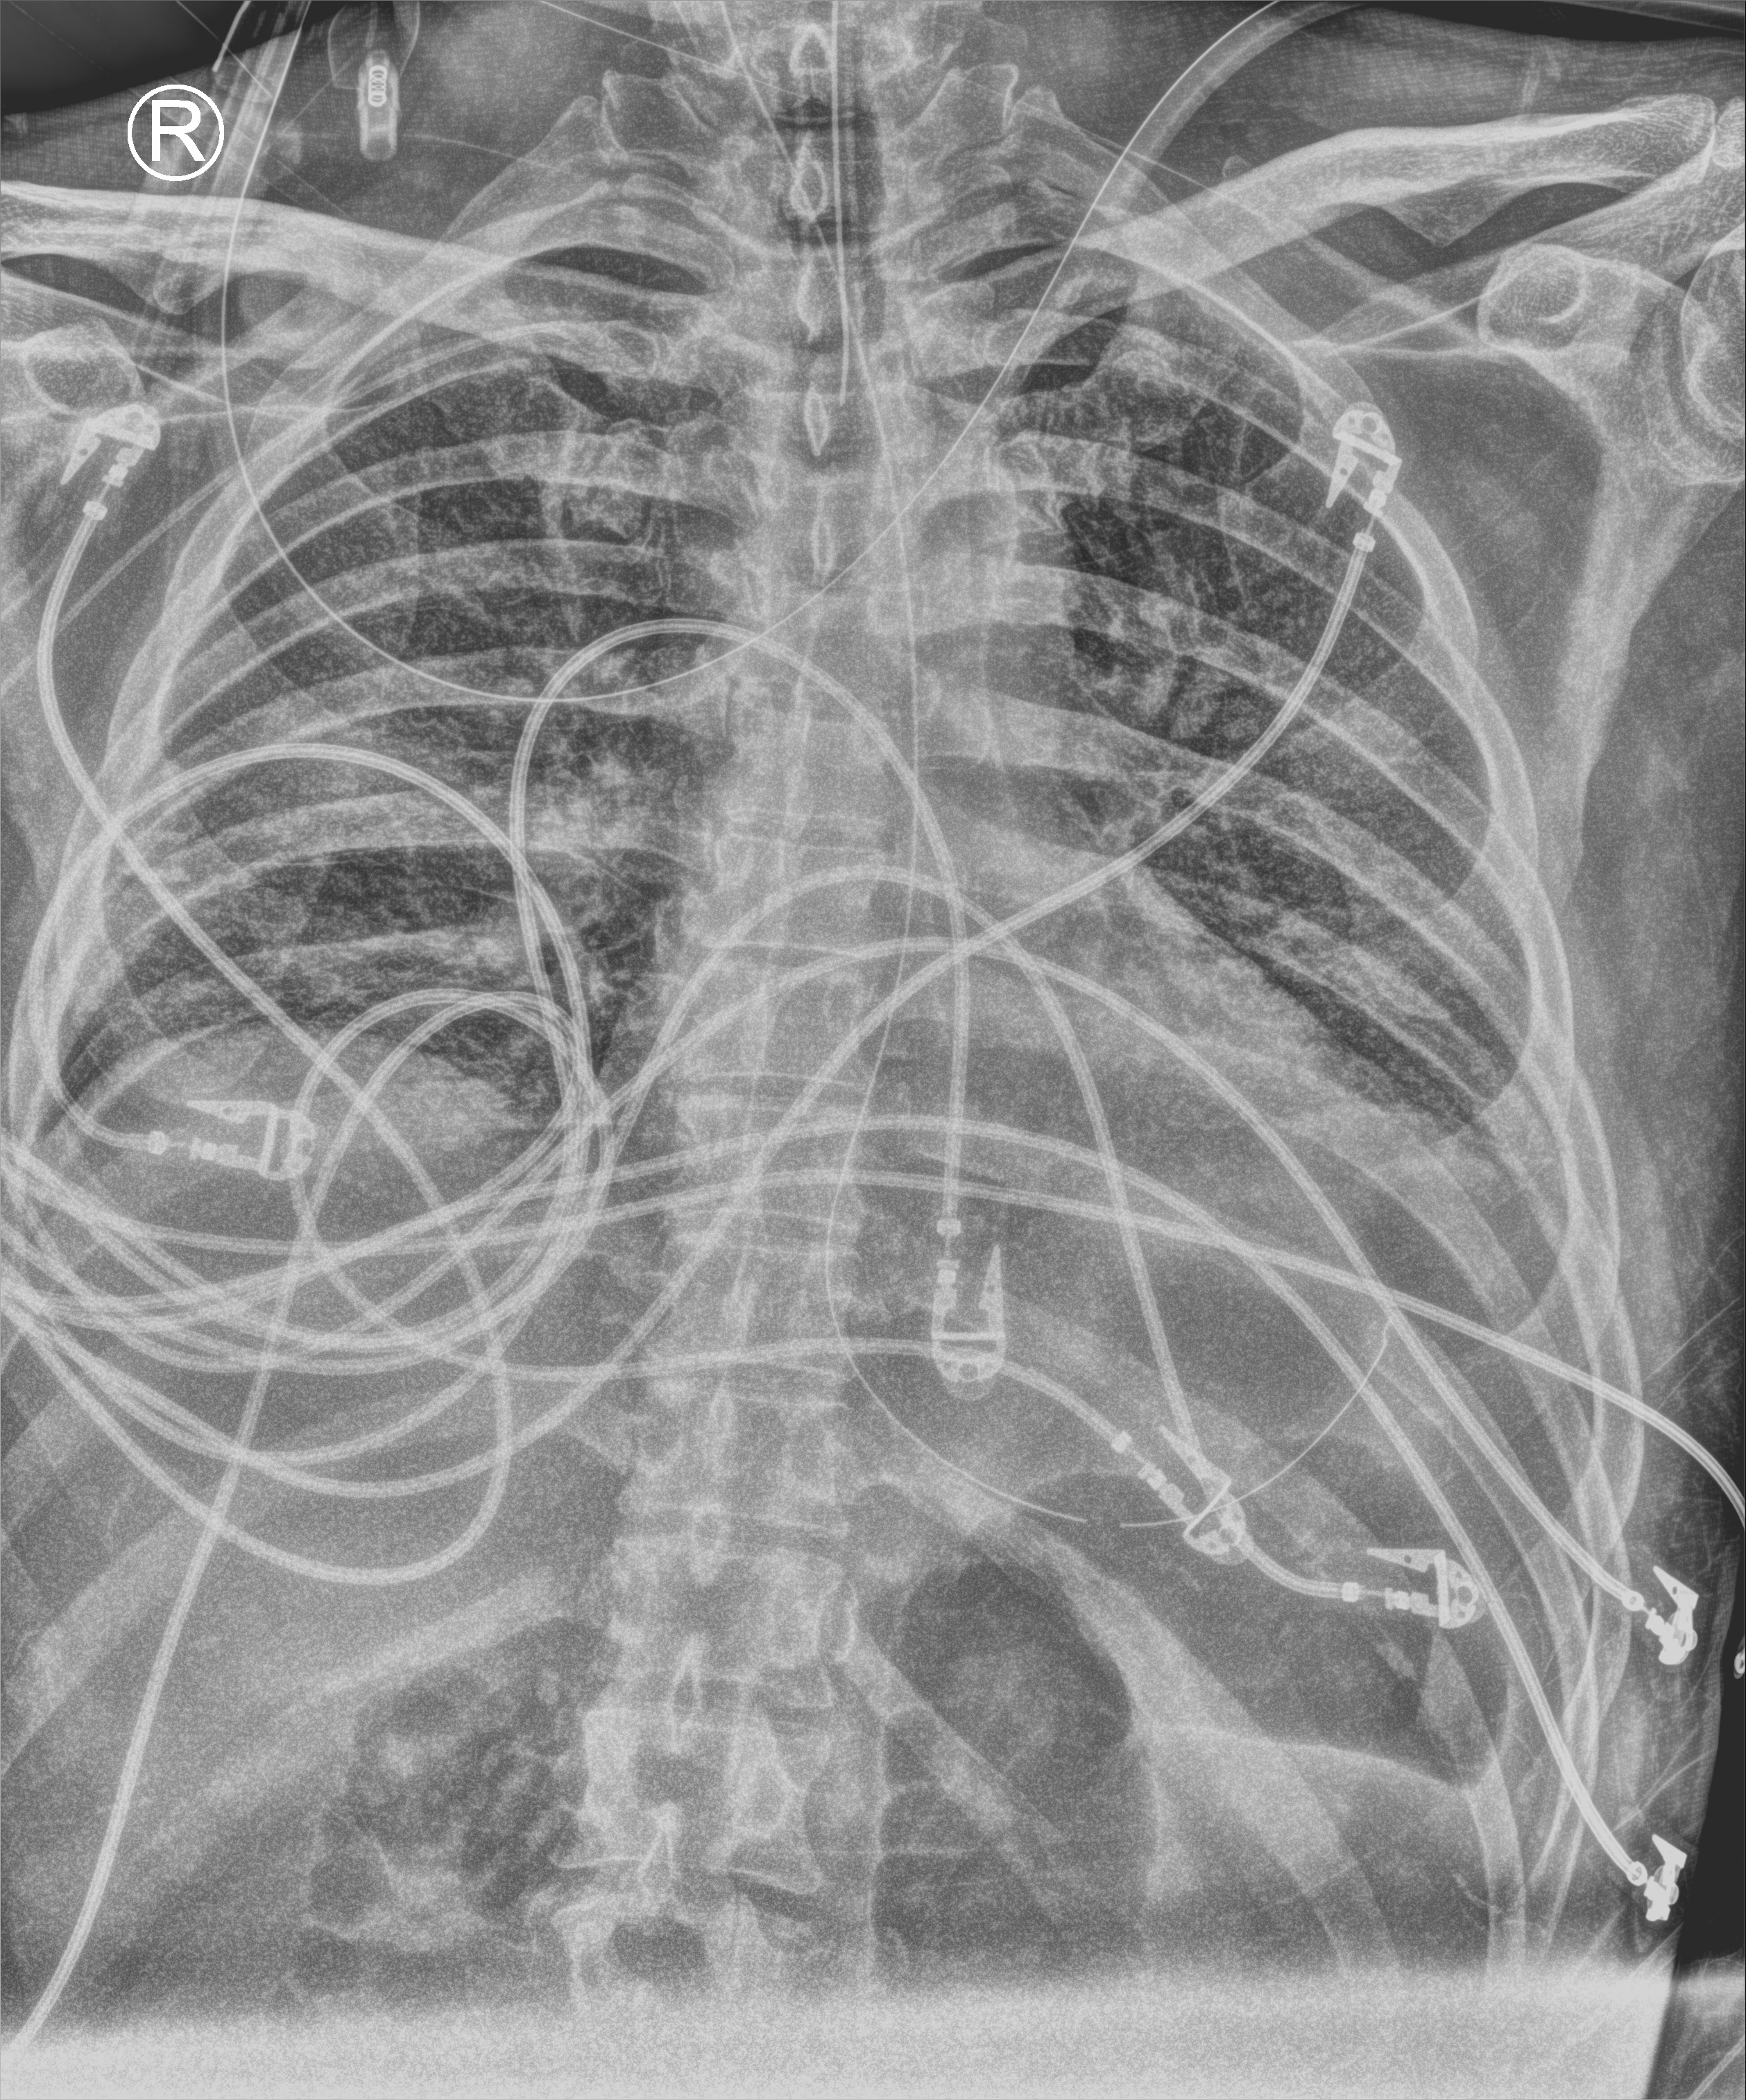
Bedside chest radiograph (computed radiography); anteroposterior (AP) projection. Male patient hospitalised with COVID-19, age 60–74 years.
From the hospital-stay record, not from the radiograph (when in the stay this image was taken is not recorded):
- length of hospital stay: 26 days
- mechanically ventilated during this hospital stay: yes